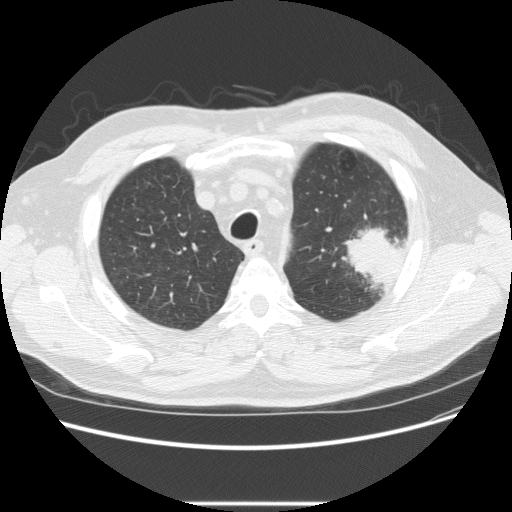
Chest CT (low-dose screening protocol), one axial image, baseline screening round, lung window (W 1500 / L -600 HU), 2.5 mm slice thickness, standard (soft-tissue) reconstruction kernel (STANDARD). Male, age 73 years at enrolment. Former smoker at enrolment.
Expert reader's lesion annotation, bounding box [x1, y1, x2, y2] px = [332, 216, 412, 285]. The screening reader recorded 2 non-calcified nodules or masses ≥4 mm on this exam; which of them this box marks is not recorded. Participant outcome: lung cancer diagnosed 11 days after this screen — bronchiolo-alveolar adenocarcinoma, NOS, other location, well differentiated (G1), stage IV (AJCC 6th edition).